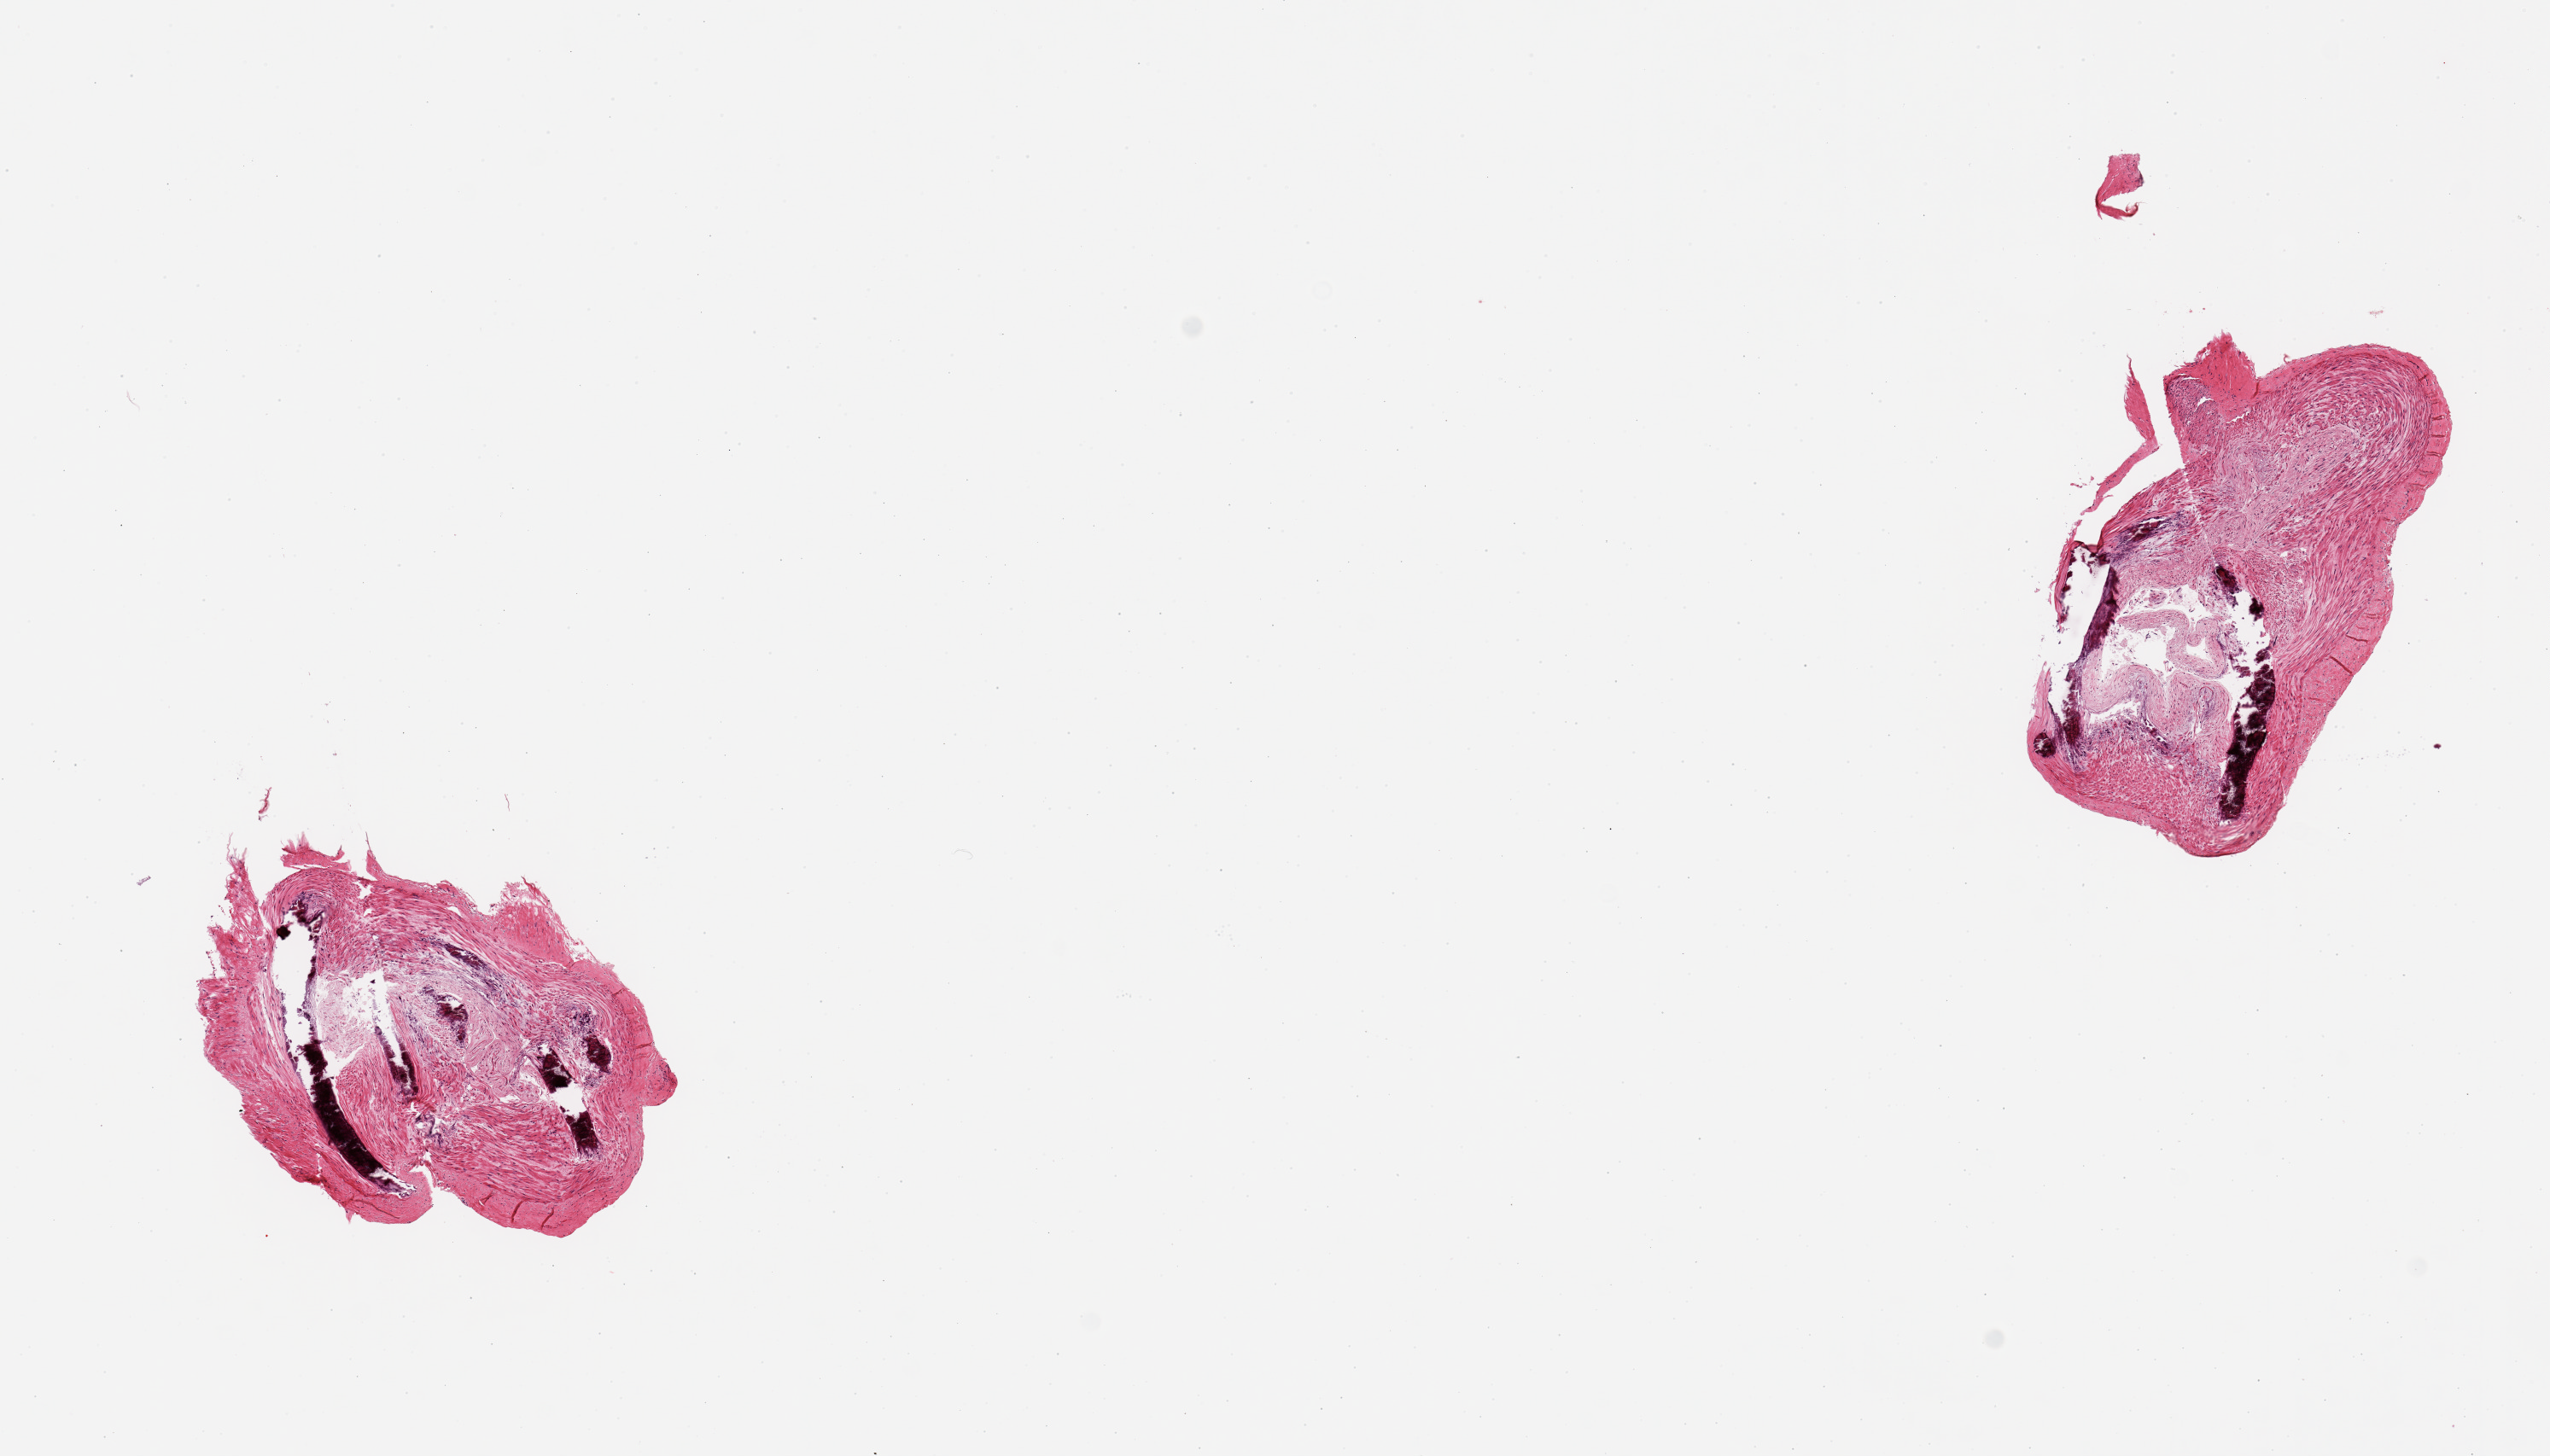
Whole-slide image, haematoxylin and eosin stain, a low-resolution overview of the entire scanned area, about 11.8 x 6.7 mm (slide scanned at 20x). PAXgene-fixed, paraffin-embedded tissue. Section of tibial artery (target tissue). Tissue donor sample. Male donor.
Reviewer comment on this tissue sample: 2 pieces, extensive Monckeberg sclerosis.